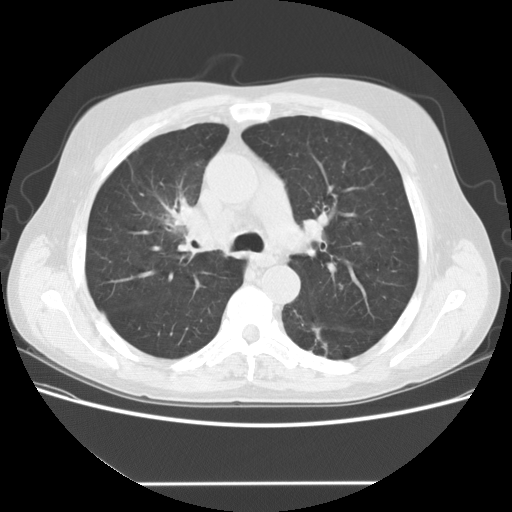
Low-dose screening chest CT, one axial slice; position 103 of 153 along the scan axis; 120 kVp; lung window (W 1500 / L -600 HU); 2.5 mm slice thickness; 512 × 512 image matrix, field of view 360 × 360 mm.
Annotated regions visible in this slice (outlined manually by an expert reader):
- lesion 1 (tumor, upper lobe of right lung): bounding box [x1, y1, x2, y2] px = [168, 197, 200, 225]